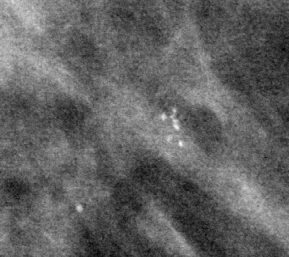
Region of interest cut from a scanned film mammogram (one marked finding); right breast; CC view.
- Calcifications, morphology pleomorphic, distribution clustered; BI-RADS assessment category 4; pathology (as recorded): benign.